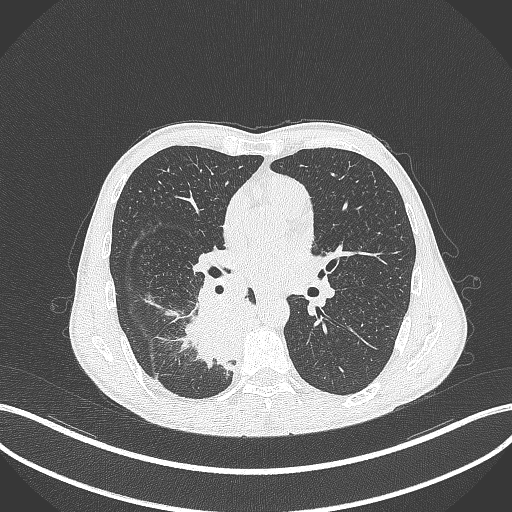
Chest CT, one axial slice. Slice 193 of 371 in the series (ordered by position). 120 kVp. Lung window (W 1500 / L -600 HU). 512 × 512 image matrix, field of view 400 × 400 mm. Male patient, age 58 years. From the clinical record (not read from this slice): clinical TNM (as recorded): T3 N1 M1.
Annotated regions visible in this slice (bounding box drawn by a radiologist):
- lung tumour (recorded histology: squamous cell carcinoma): box from (x=181, y=275) to (x=268, y=372) px